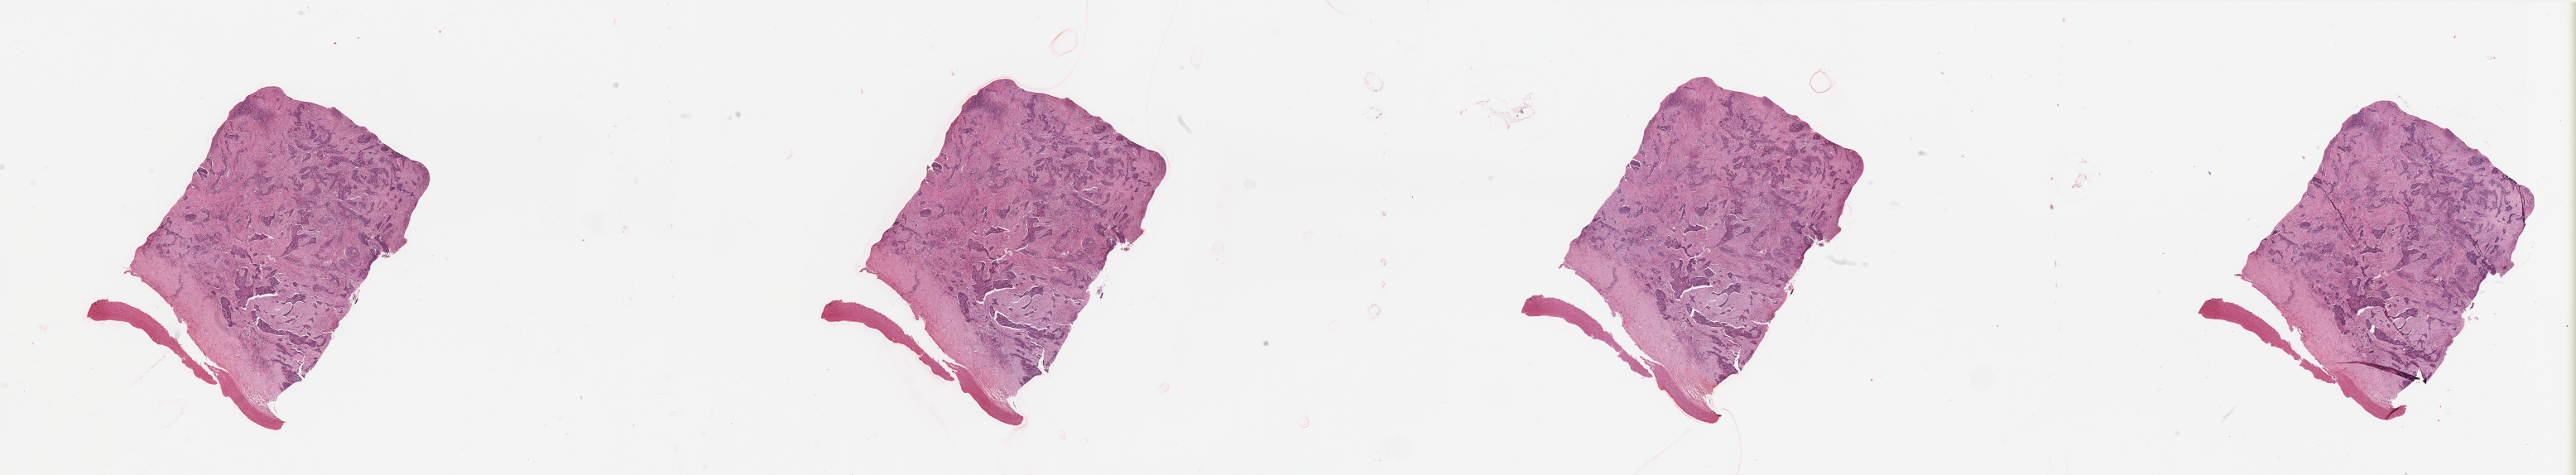
Digitized H&E tissue section (whole slide) — whole scanned area (about 49.2 x 9.1 mm) shown as a low-resolution overview; tumour tissue sample, sampled site: lung. Patient: male, age 73 years. Histologic grade: G2 (moderately differentiated). Composition of this section per pathologist review: tumour nuclei 65%, necrosis 0%.
AJCC pathologic stage: II. Diagnosis: Squamous cell carcinoma, NOS. Primary tumour site (as recorded): right middle lobe.